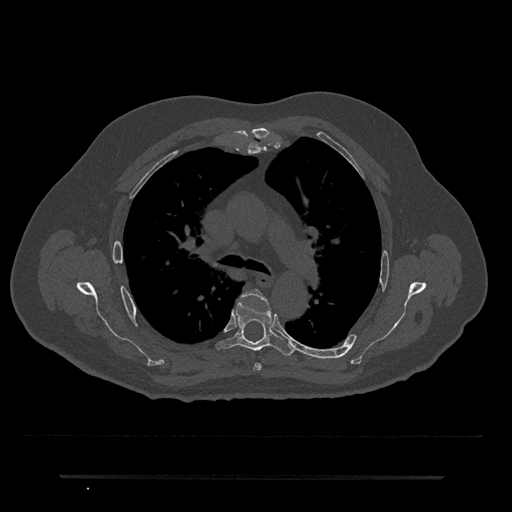
CT including the spine, one axial slice. 120 kVp. Bone window (W 1800 / L 400 HU). 512 × 512 image matrix, field of view 437 × 437 mm. Patient: male, 69 years. From the clinical record (not read from this slice): primary cancer: prostate.
Structures marked on this image (semi-automatically segmented with operator editing):
- T4 vertebra: bounding box (x1, y1, x2, y2) in pixels: (242, 289, 268, 371)
- T5 vertebra: (216, 297, 294, 355)